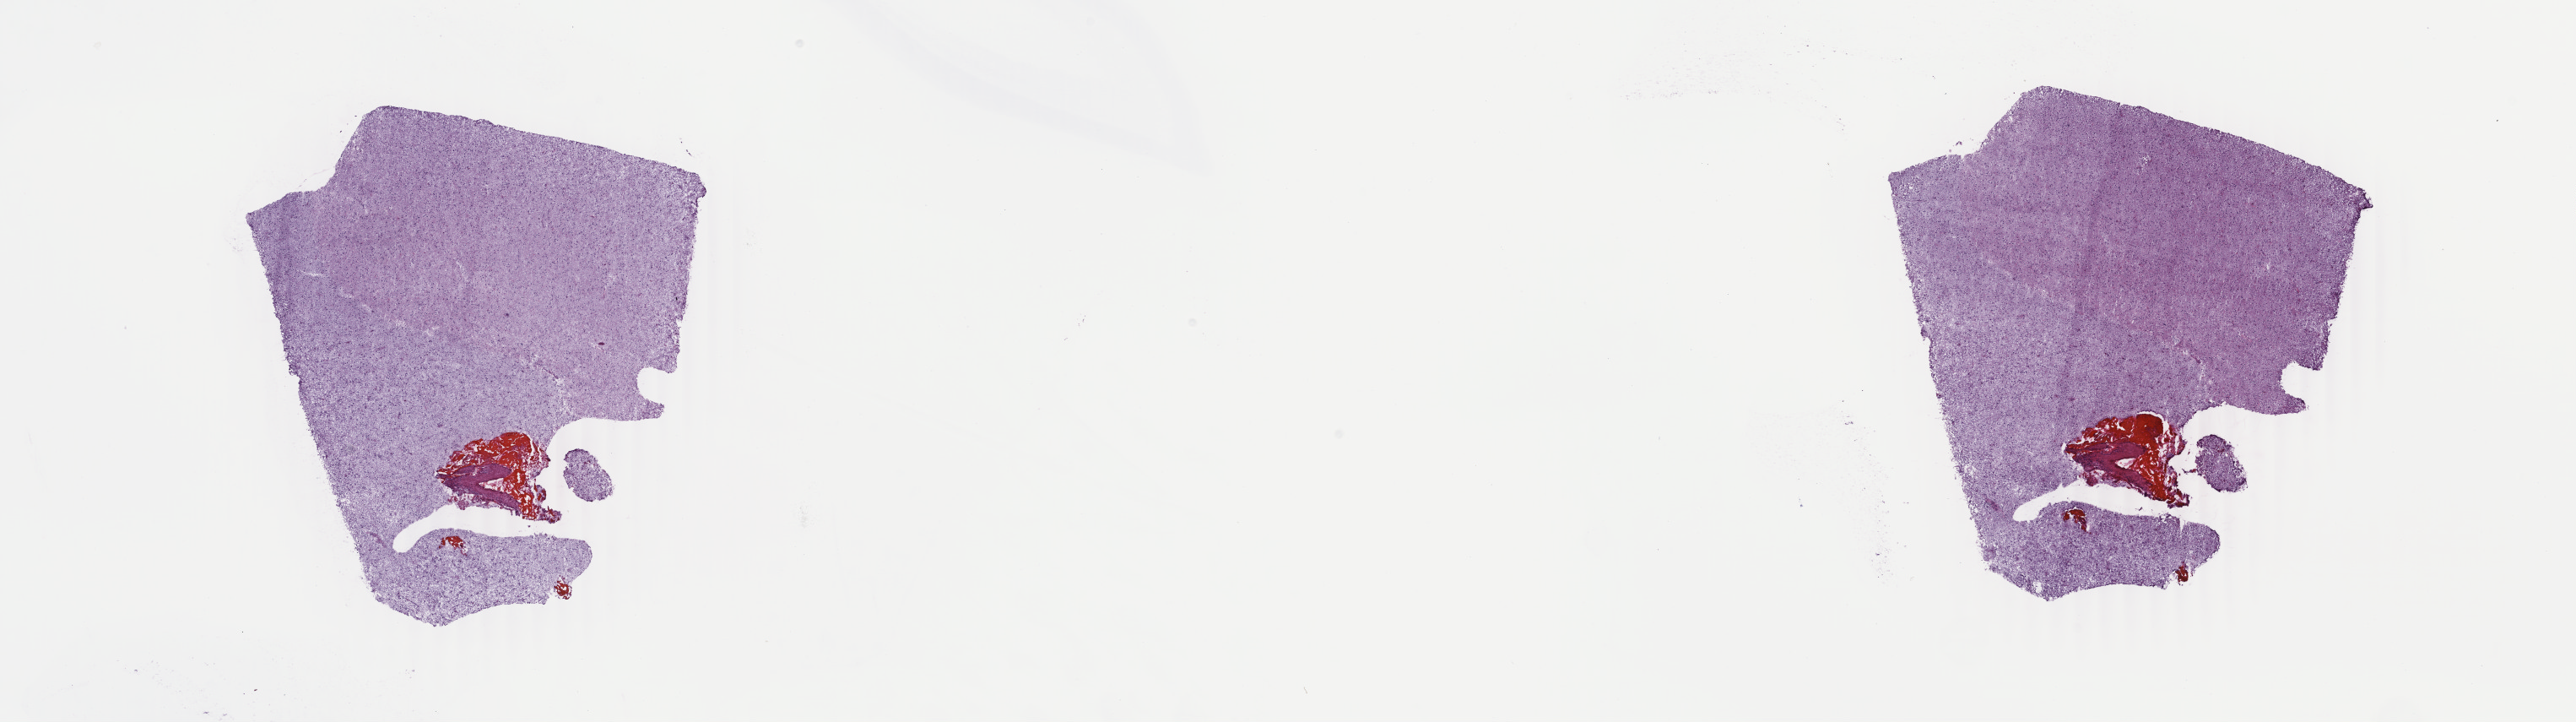
Digitized H&E tissue section (whole slide), low-resolution overview of the scanned area, about 24.3 x 6.8 mm (from a 40x scan). Frozen section from the top of the tissue portion. Brain, primary tumour sample. Male patient; age at initial diagnosis 58 years. Histologic grade: G3 (poorly differentiated). Slide review estimates, as recorded: tumour cells 40%, tumour nuclei 80%, normal cells 10%, stromal cells 50%, necrosis 0%. Infiltration values recorded for this section: lymphocyte infiltration 0%, monocyte infiltration 0%, neutrophil infiltration 0%.
• histologic diagnosis: Astrocytoma, anaplastic (cerebrum)